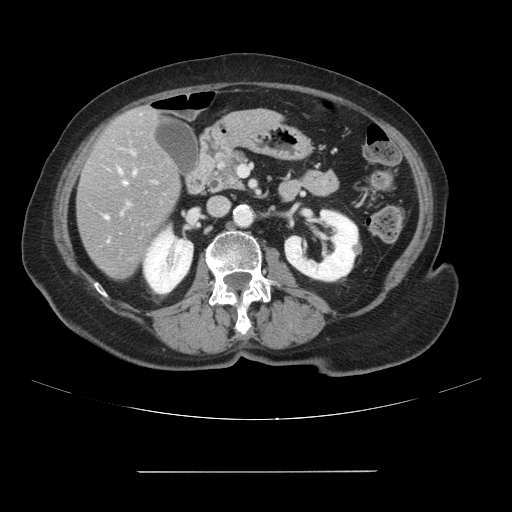
Contrast-enhanced abdominal CT, one axial slice; slice 33 of 111 in the series (ordered by position); 120 kVp; intravenous contrast given; soft-tissue window (W 400 / L 40 HU); 2.5 mm slice thickness; 512 × 512 image matrix, field of view 400 × 400 mm. Female patient, age 74 years. Case-level facts recorded for this patient, not image findings: diagnosis: colorectal cancer liver metastases, imaged before liver resection; multiple liver metastases: yes; largest metastasis: 1.1 cm; disease in both lobes: yes.
Annotated regions visible in this slice (outlined manually by an expert reader):
- hepatic veins: bounding box <120,171,126,184> (left, top, right, bottom; pixels)
- liver: <78,107,276,280>
- planned liver remnant (the part of the liver to remain after resection): <141,107,256,128>